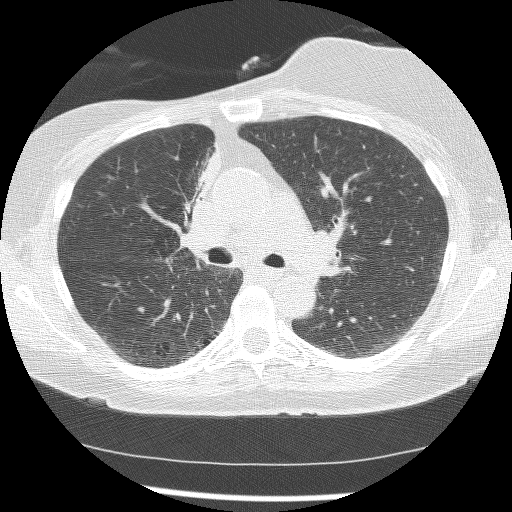
Low-dose screening chest CT, axial slice, first (baseline) screen, lung window (W 1500 / L -600 HU), 2.5 mm slice thickness, lung (sharp) reconstruction kernel (BONE), slice 59 of 172 in the series. Female, age 56 years at enrolment. Current smoker at enrolment.
Expert reader's lesion annotation, bounding box <162,150,217,259> (left, top, right, bottom; pixels). The screening reader recorded 2 non-calcified nodules or masses ≥4 mm on this exam (right lower lobe, right middle lobe); which of them this box marks is not recorded. Official screen result: positive, change unspecified: nodule(s) >= 4 mm or enlarging nodule(s), mass(es), or other non-specific abnormalities suspicious for lung cancer. Later outcome: lung cancer diagnosed 1185 days after this screen — adenocarcinoma, NOS, right upper lobe, stage IIIB (AJCC 6th edition), 8 mm at pathology.